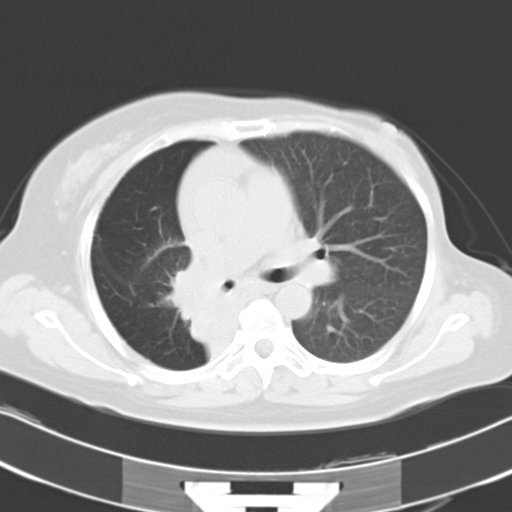
Chest CT, one axial slice. Slice 19 of 30 in the series (ordered by position). Reconstruction kernel B40f. 120 kVp. Lung window (W 1500 / L -600 HU). 8 mm slice thickness. 512 × 512 image matrix, field of view 331 × 331 mm. Patient: female, 53 years. From the clinical record (not read from this slice): clinical TNM (as recorded): T2b N1 M0.
Annotated regions visible in this slice (bounding box drawn by a radiologist):
- lung tumour (recorded histology: adenocarcinoma): bounding box [x1, y1, x2, y2] px = [166, 256, 226, 340]